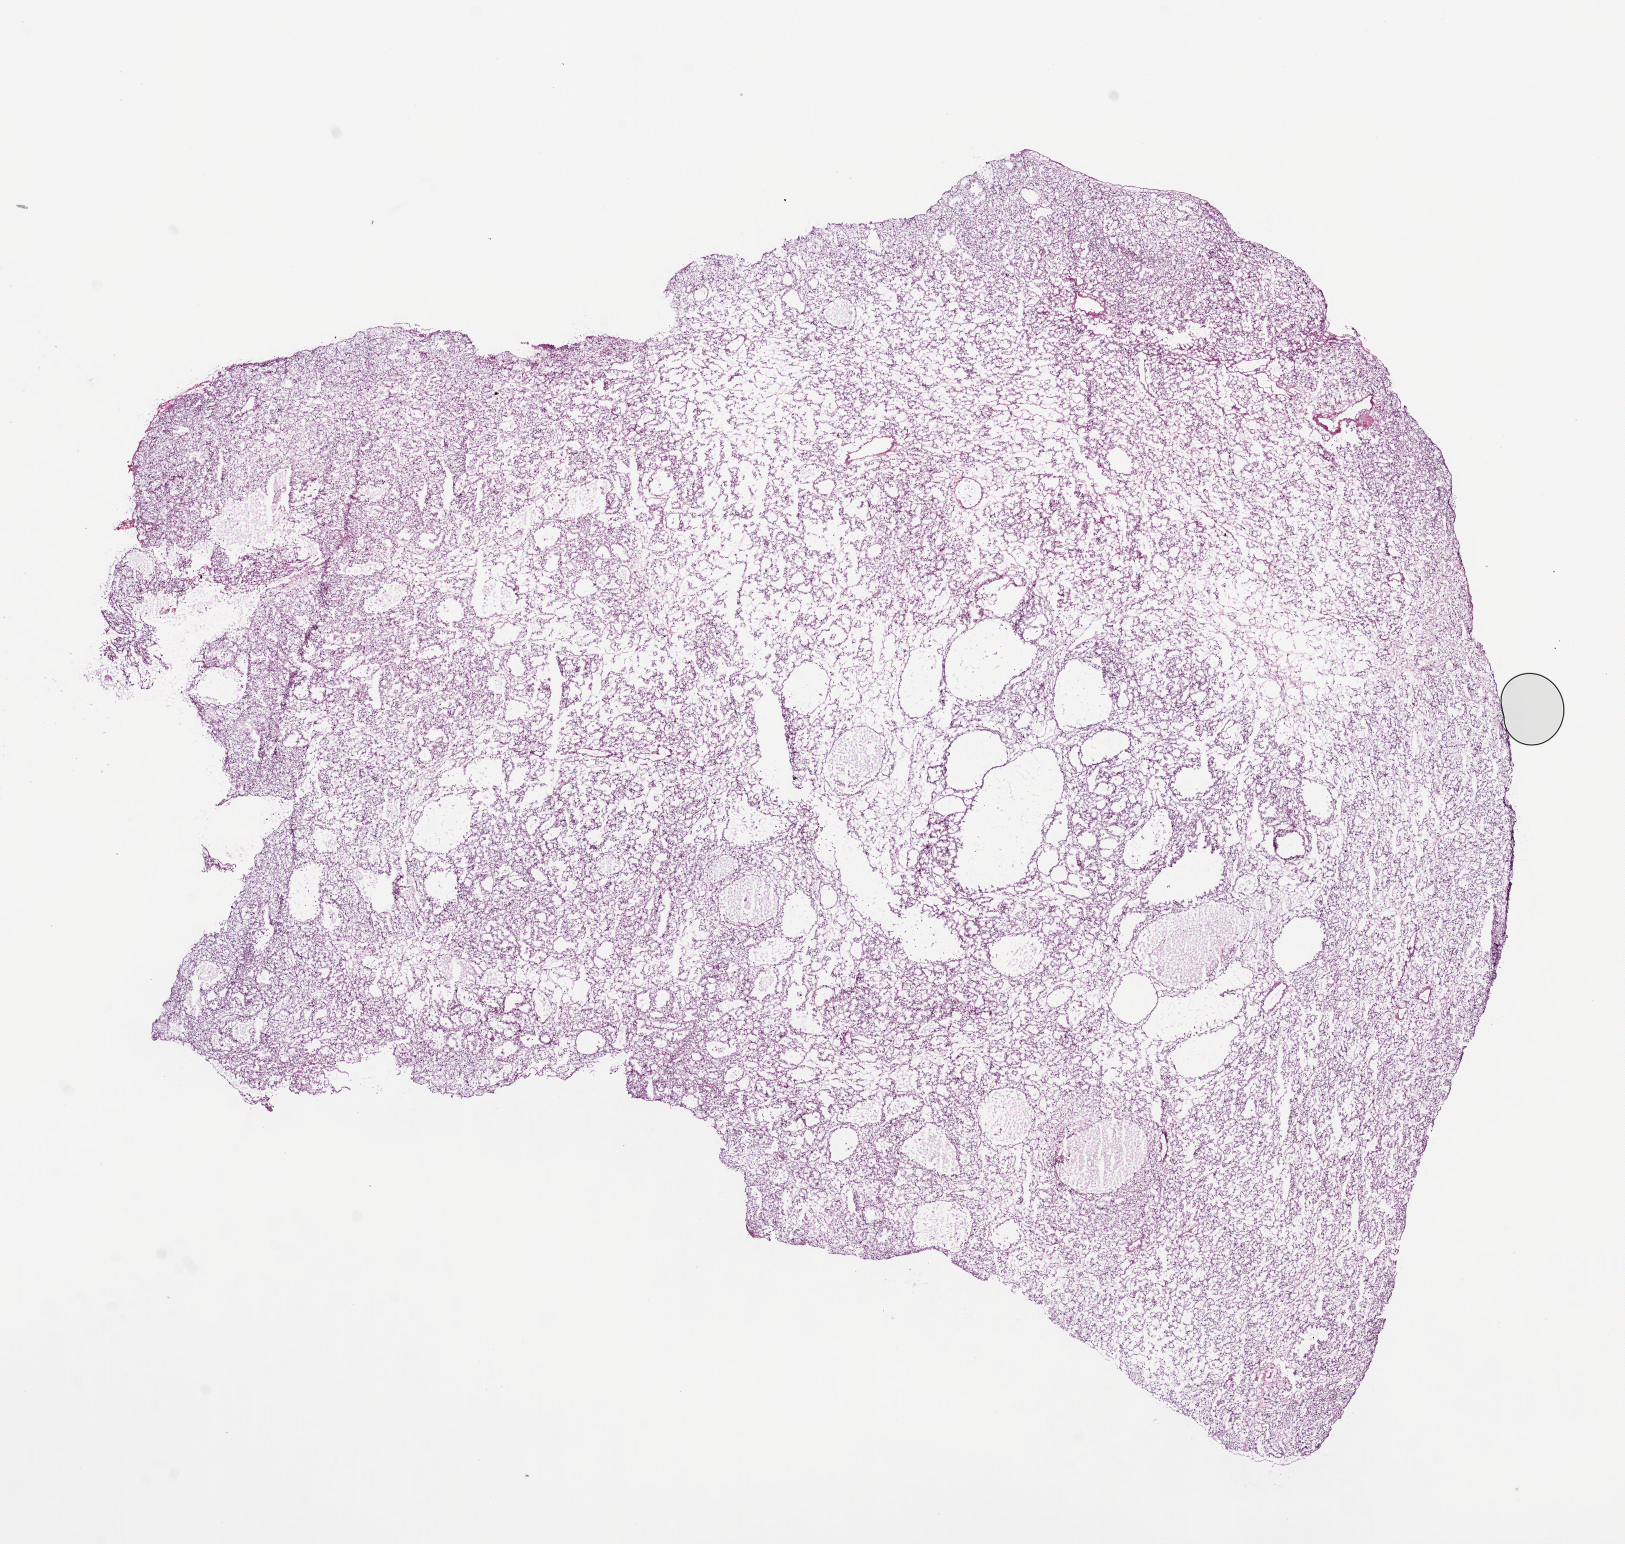
Digitized Hematoxylin and eosin (H&E) stained tissue section (whole slide), a low-resolution overview of the entire scanned area, about 13.0 x 12.4 mm (slide scanned at 20x), frozen section, kidney, primary tumour sample. Male patient; age at initial diagnosis 75 years. Histologic grade: G2 (moderately differentiated). Slide review estimates, as recorded: tumour cells 95%, tumour nuclei 90%, normal cells 0%, stromal cells 5%, necrosis 0%.
Histologic diagnosis: Clear cell adenocarcinoma, NOS. AJCC pathologic stage: III. Laterality: right.